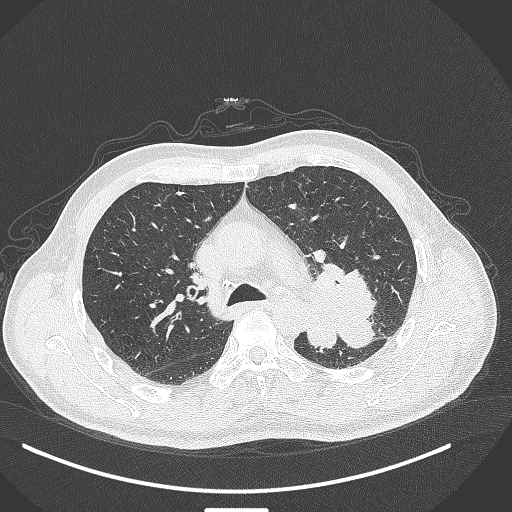
Chest CT, one axial slice. Position 281 of 429 along the scan axis. 120 kVp. Lung window (W 1500 / L -600 HU). 1 mm slice thickness. 512 × 512 image matrix. Male patient, age 55 years. From the clinical record (not read from this slice): clinical TNM (as recorded): T3 N0 M1c.
Annotated regions visible in this slice (bounding box drawn by a radiologist):
- lung tumour (recorded histology: adenocarcinoma): bounding box [x1, y1, x2, y2] px = [305, 257, 376, 358]